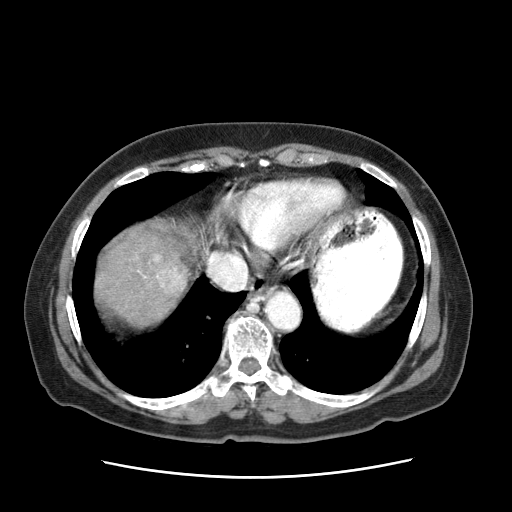
Contrast-enhanced abdominal CT (liver protocol), one axial slice. Slice 60 of 63 in the series (ordered by position). Reconstruction kernel STANDARD. 120 kVp. Soft-tissue window (W 400 / L 40 HU). 512 × 512 image matrix, field of view 360 × 360 mm. Female patient, age 79 years. From the clinical record (not read from this slice): diagnosis: hepatocellular carcinoma (patient treated with transarterial chemoembolisation; whether this scan precedes or follows treatment is not stated here); TNM stage (as recorded): Stage-II; Child-Pugh class: B; tumour differentiation: well differentiated; tumour size: 5 cm.
Annotated regions visible in this slice (semi-automatic segmentation, software-assisted and operator-edited):
- abdominal aorta: box from (x=264, y=291) to (x=299, y=328) px
- liver parenchyma outside the tumour (the mass and vessels are separate outlines, so this box may not span the whole liver): (x=96, y=219)–(x=211, y=328)
- mass: (x=148, y=254)–(x=191, y=297)
- liver vessels: (x=137, y=251)–(x=248, y=291)